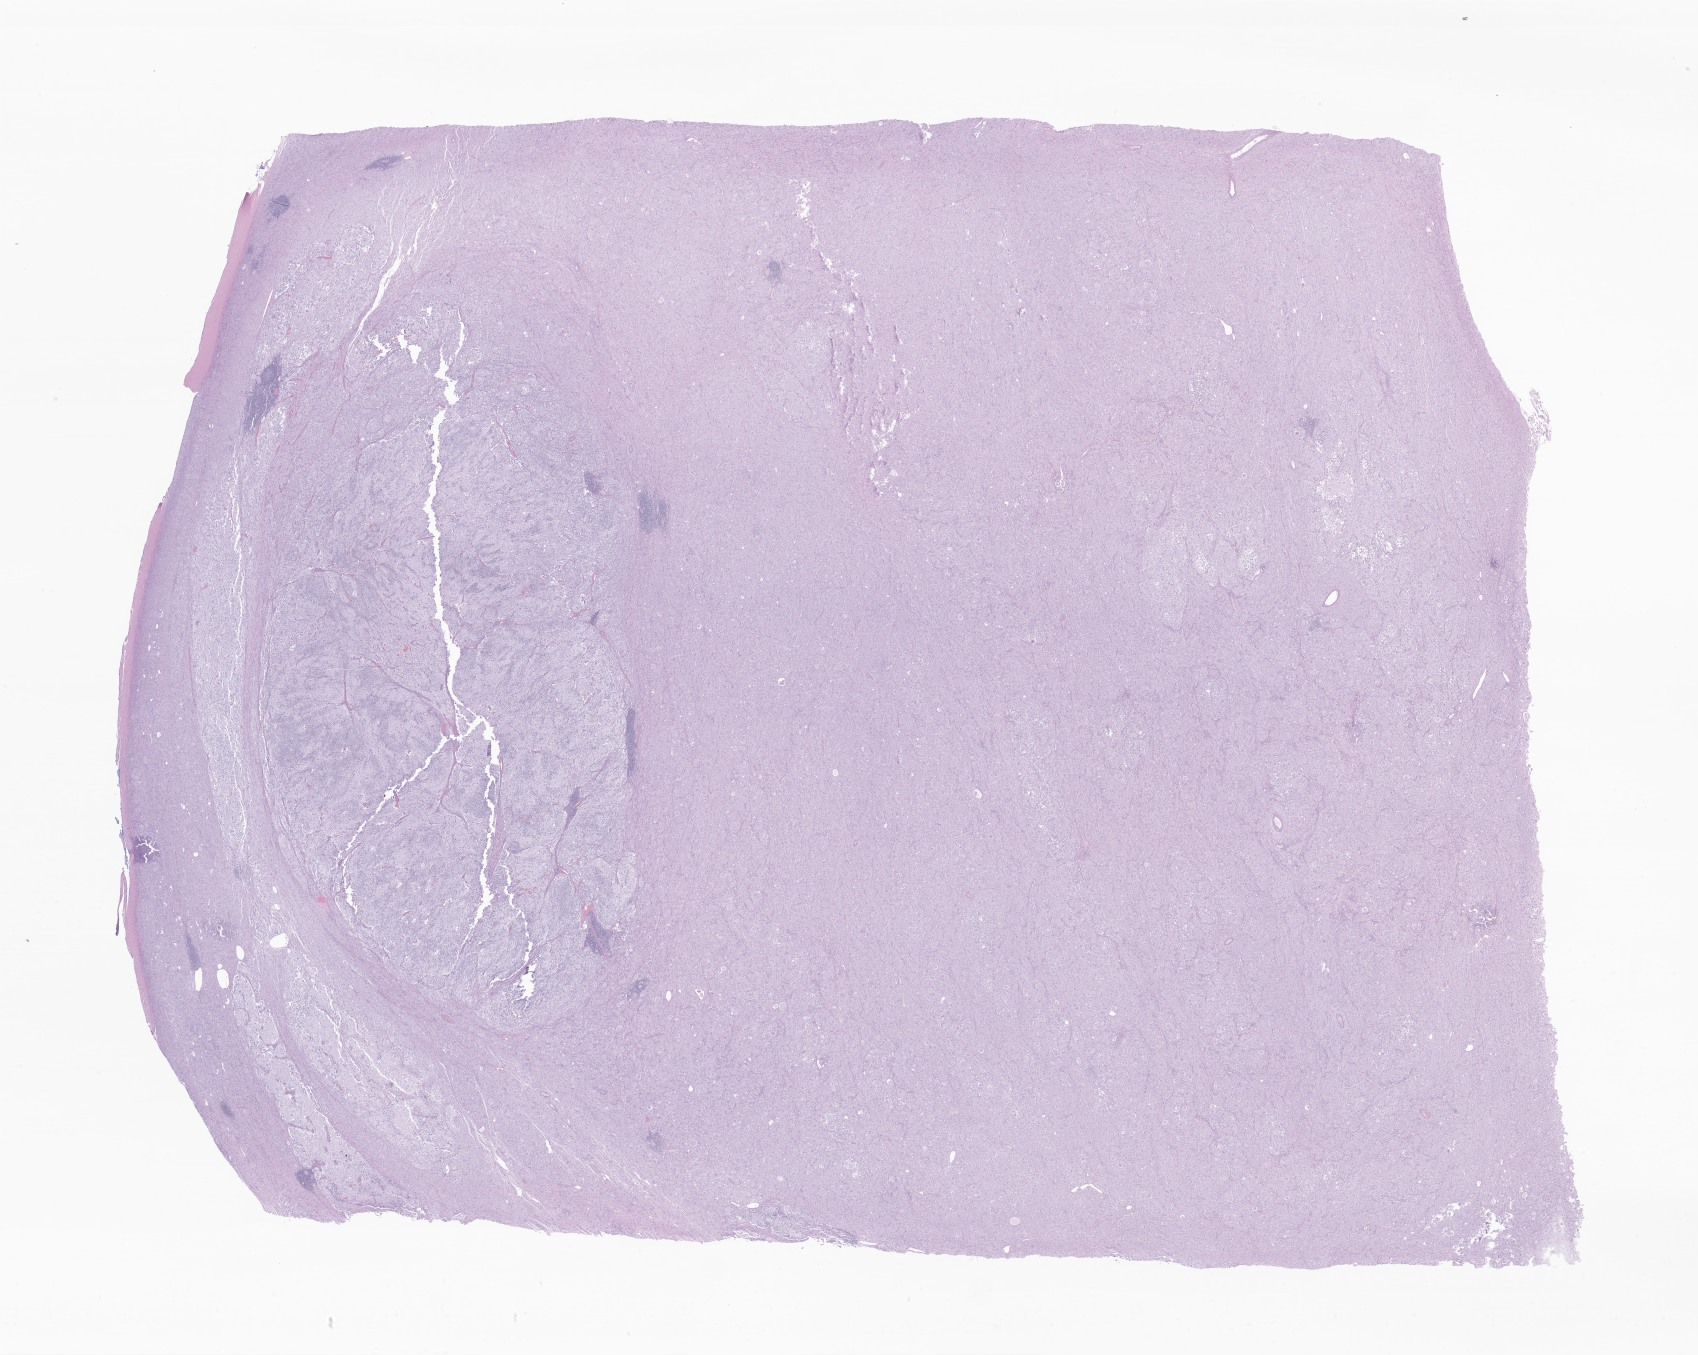
Whole-slide image, hematoxylin and eosin (H&E) stain of tumor tissue from the posterior mediastinum — low-resolution overview of the scanned area, about 28.6 x 22.9 mm; FFPE section. Female patient, age 49 months.
Recorded diagnosis: Ganglioneuroblastoma.